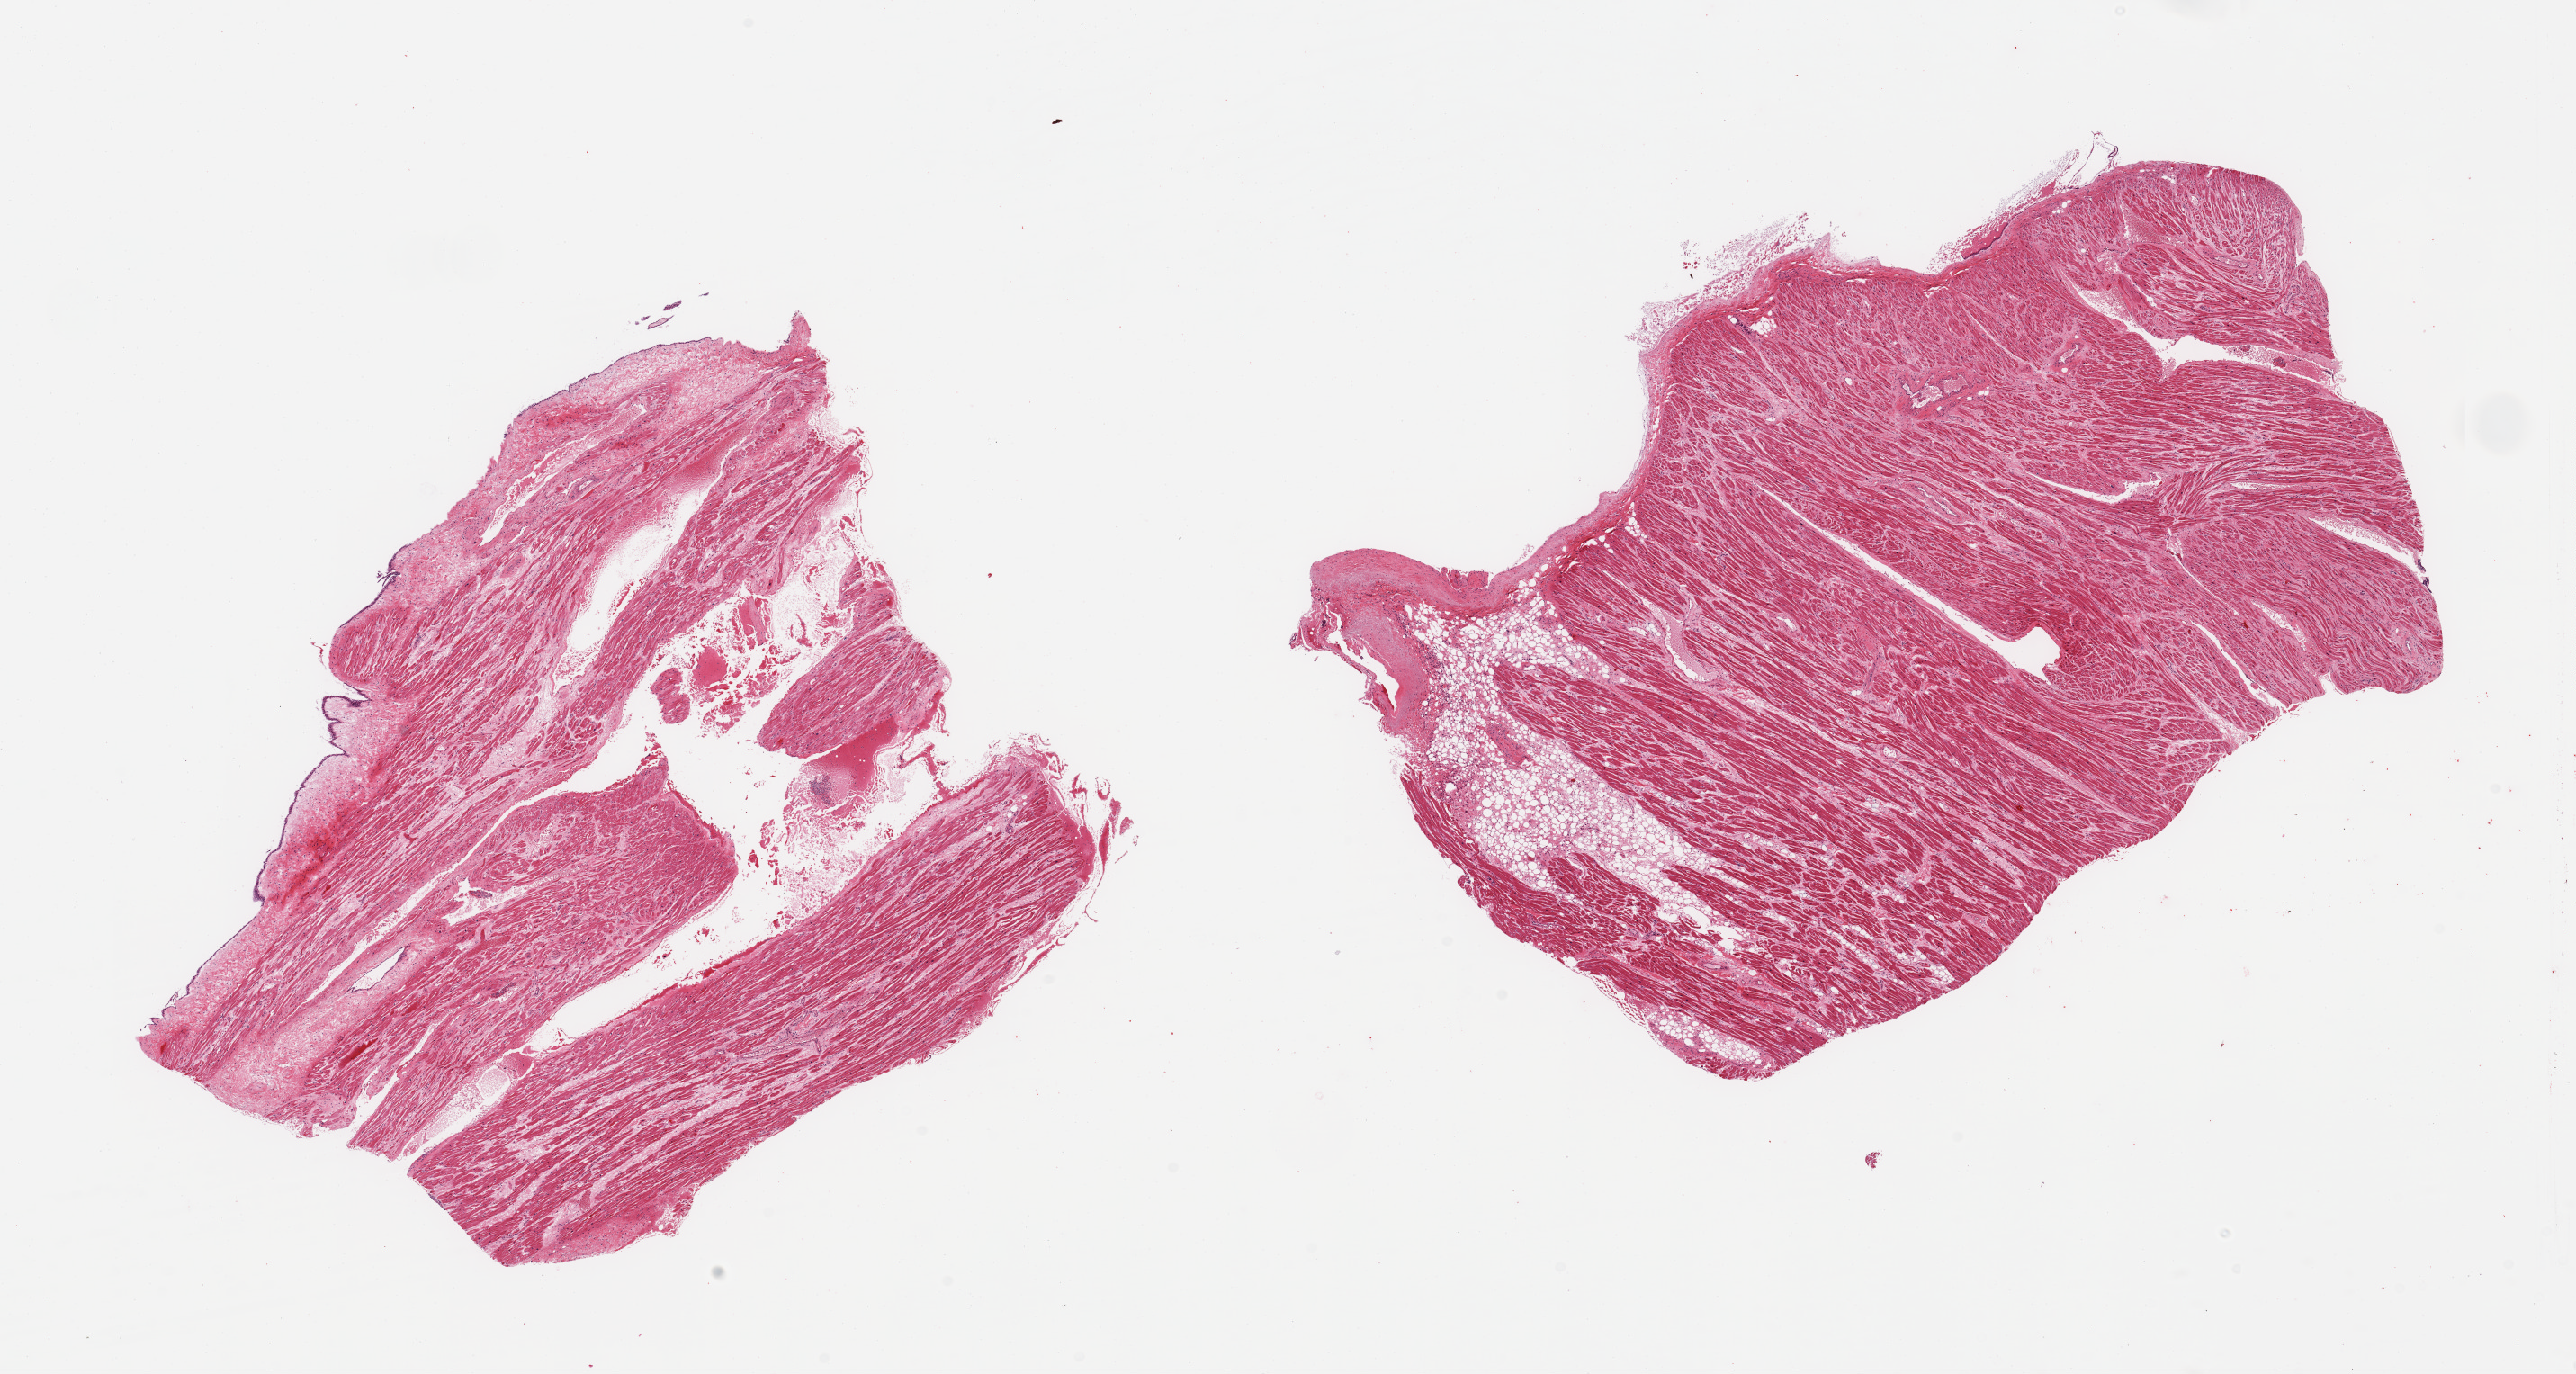
Digitized hematoxylin and eosin (H&E)-stained section, brightfield — low-resolution overview of the scanned area, about 22.6 x 12.1 mm (slide scanned at 20x), PAXgene-fixed, paraffin-embedded tissue, section of auricular appendage (target tissue), tissue donor sample. Male donor.
- pathologist's review note for this sample: 2 pieces; 20% fat & fibrous content